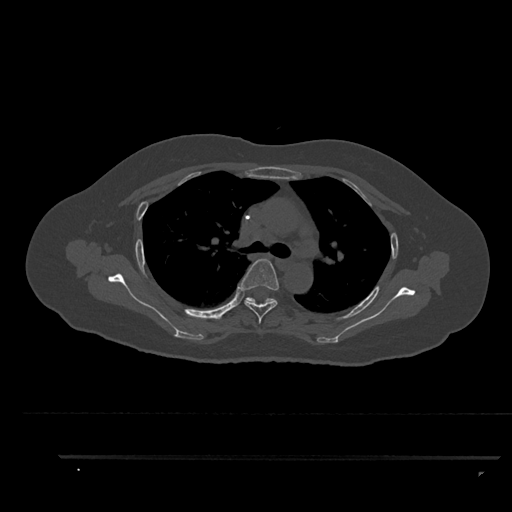
CT including the spine, one axial slice; slice 633 of 797 in the series (ordered by position); 120 kVp; bone window (W 1800 / L 400 HU); 512 × 512 image matrix, field of view 408 × 408 mm. Patient: female, 44 years. From the clinical record (not read from this slice): primary cancer: renal.
Structures marked on this image (semi-automatic segmentation, software-assisted and operator-edited):
- T4 vertebra: bounding box (x1, y1, x2, y2) in pixels: (240, 259, 279, 324)
- T5 vertebra: (244, 297, 272, 302)